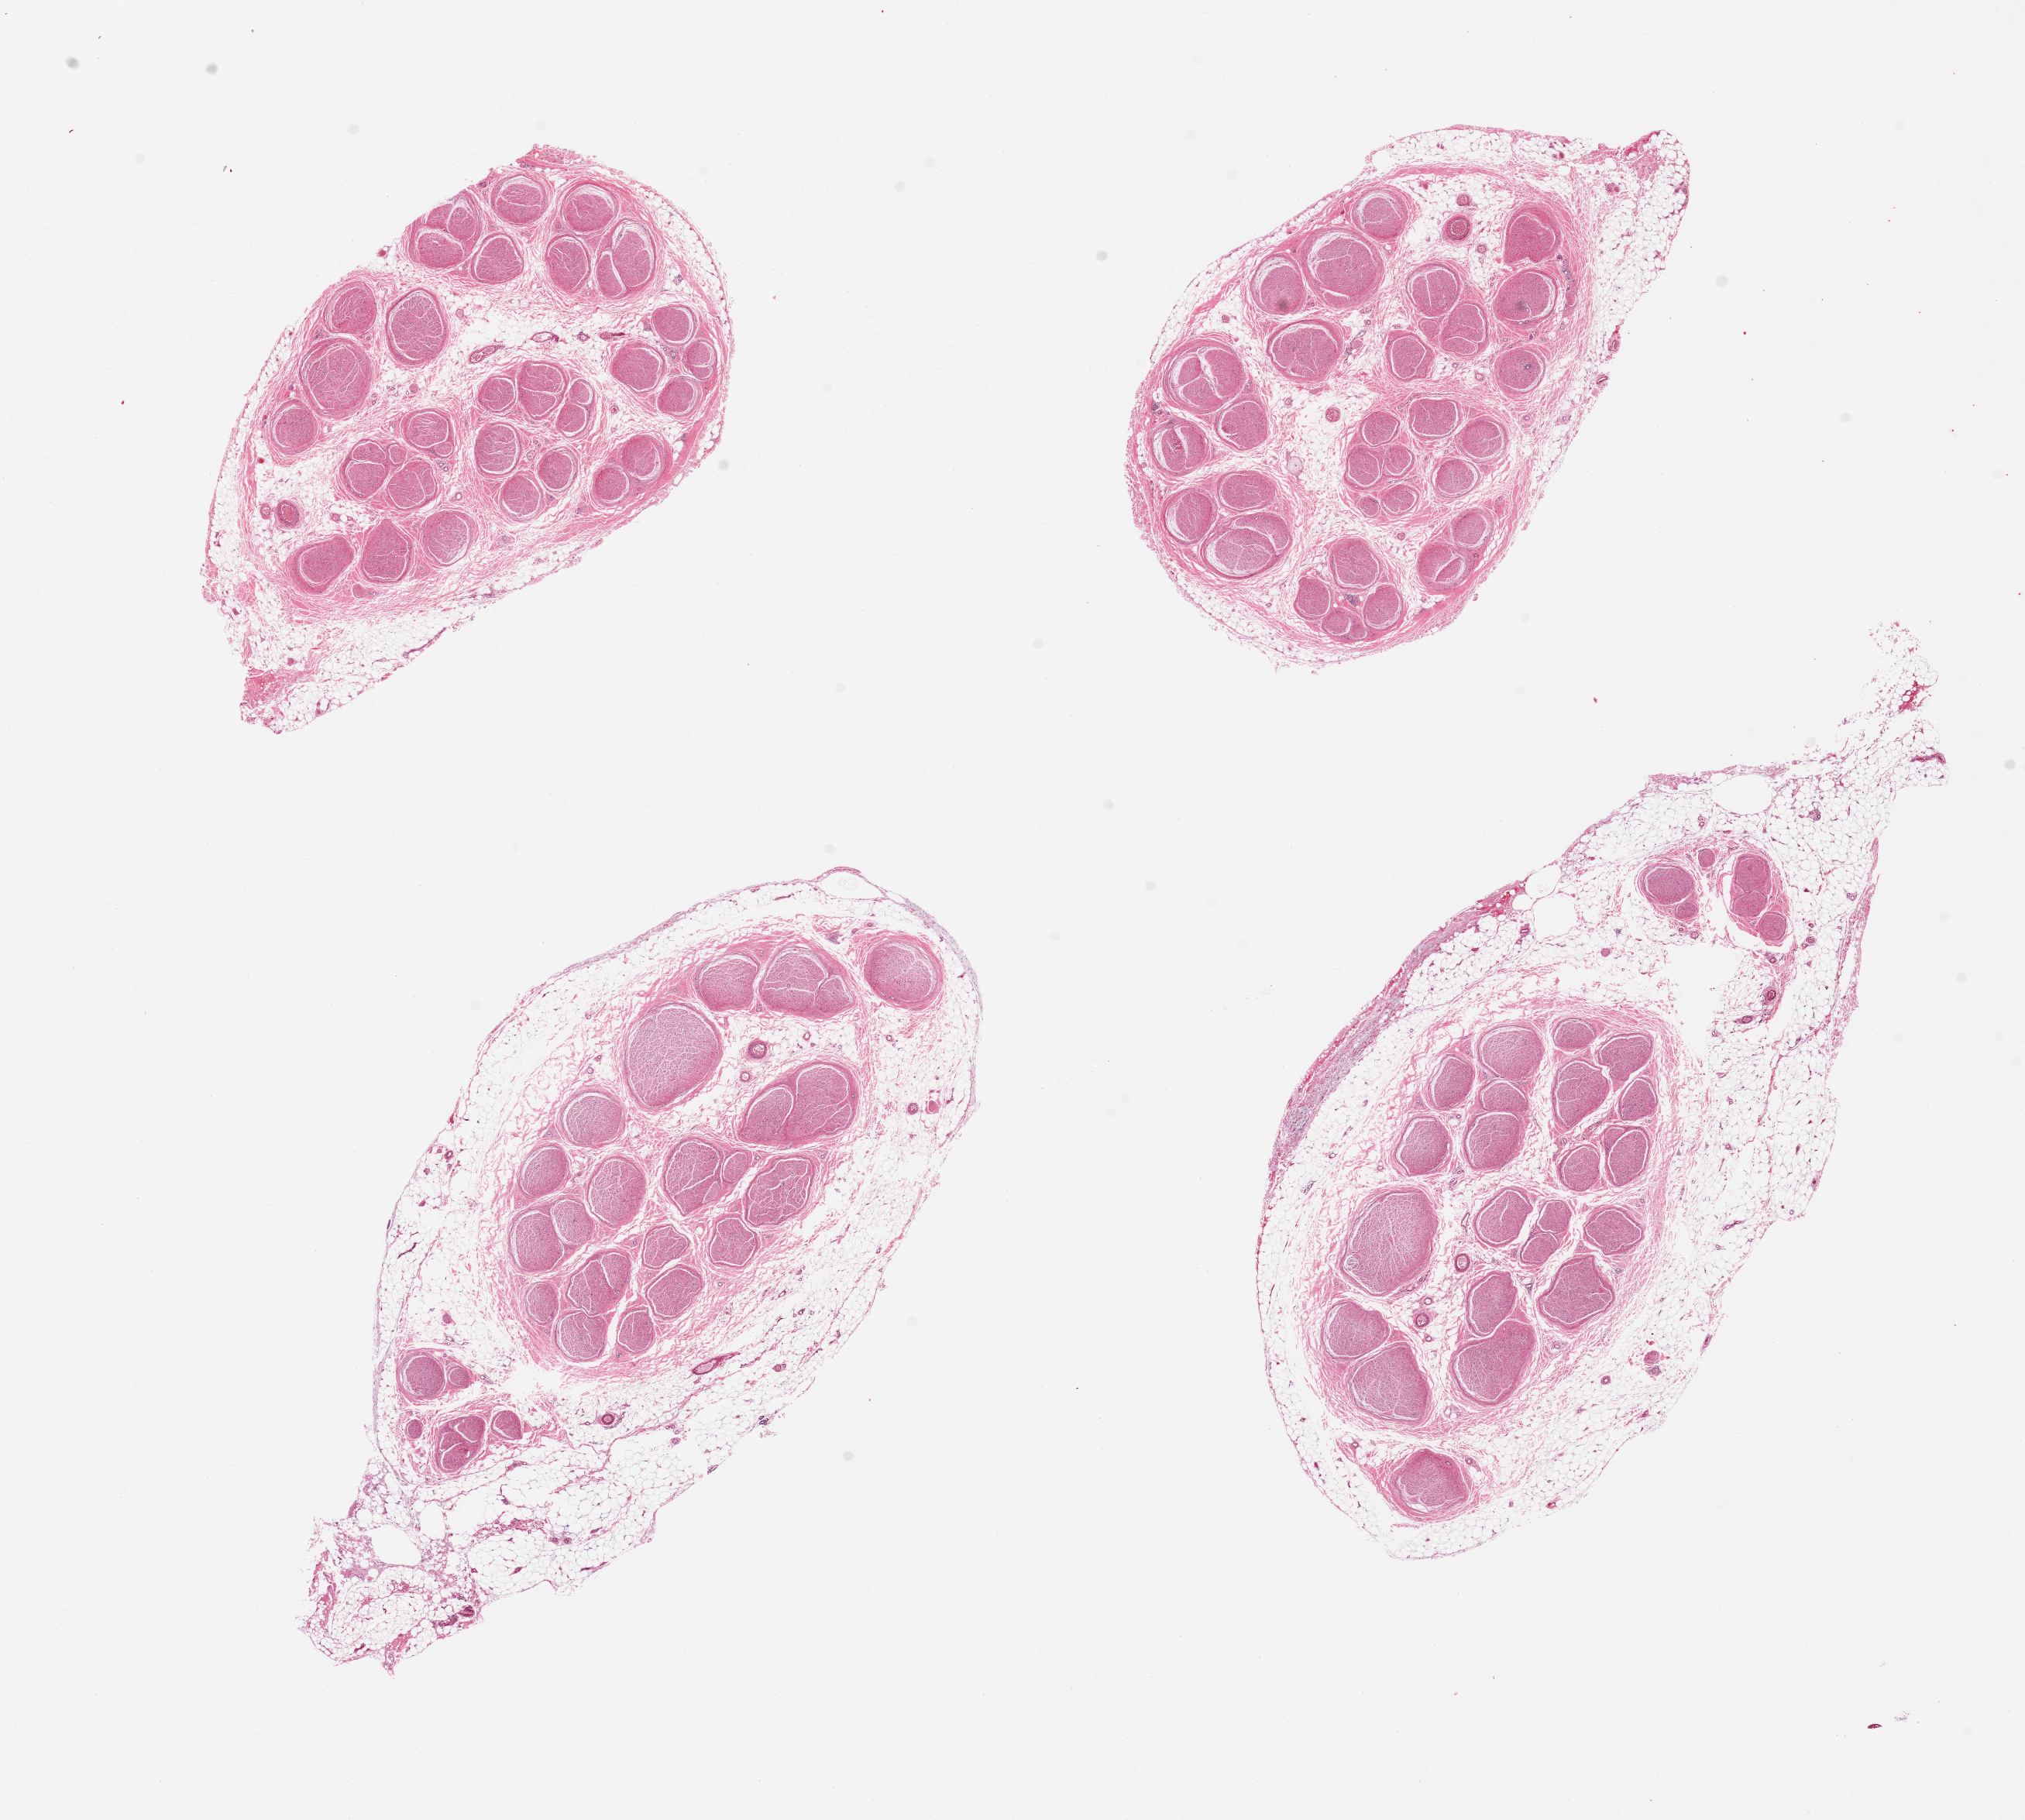
Digitized H&E-stained section — a low-resolution overview of the entire scanned area, about 20.7 x 18.6 mm, PAXgene-fixed, paraffin-embedded tissue, sampled site (target tissue): tibial nerve, donor tissue sample. Male donor.
Reviewer comment on this tissue sample: 4 pieces; up to 50% fatty envelope.